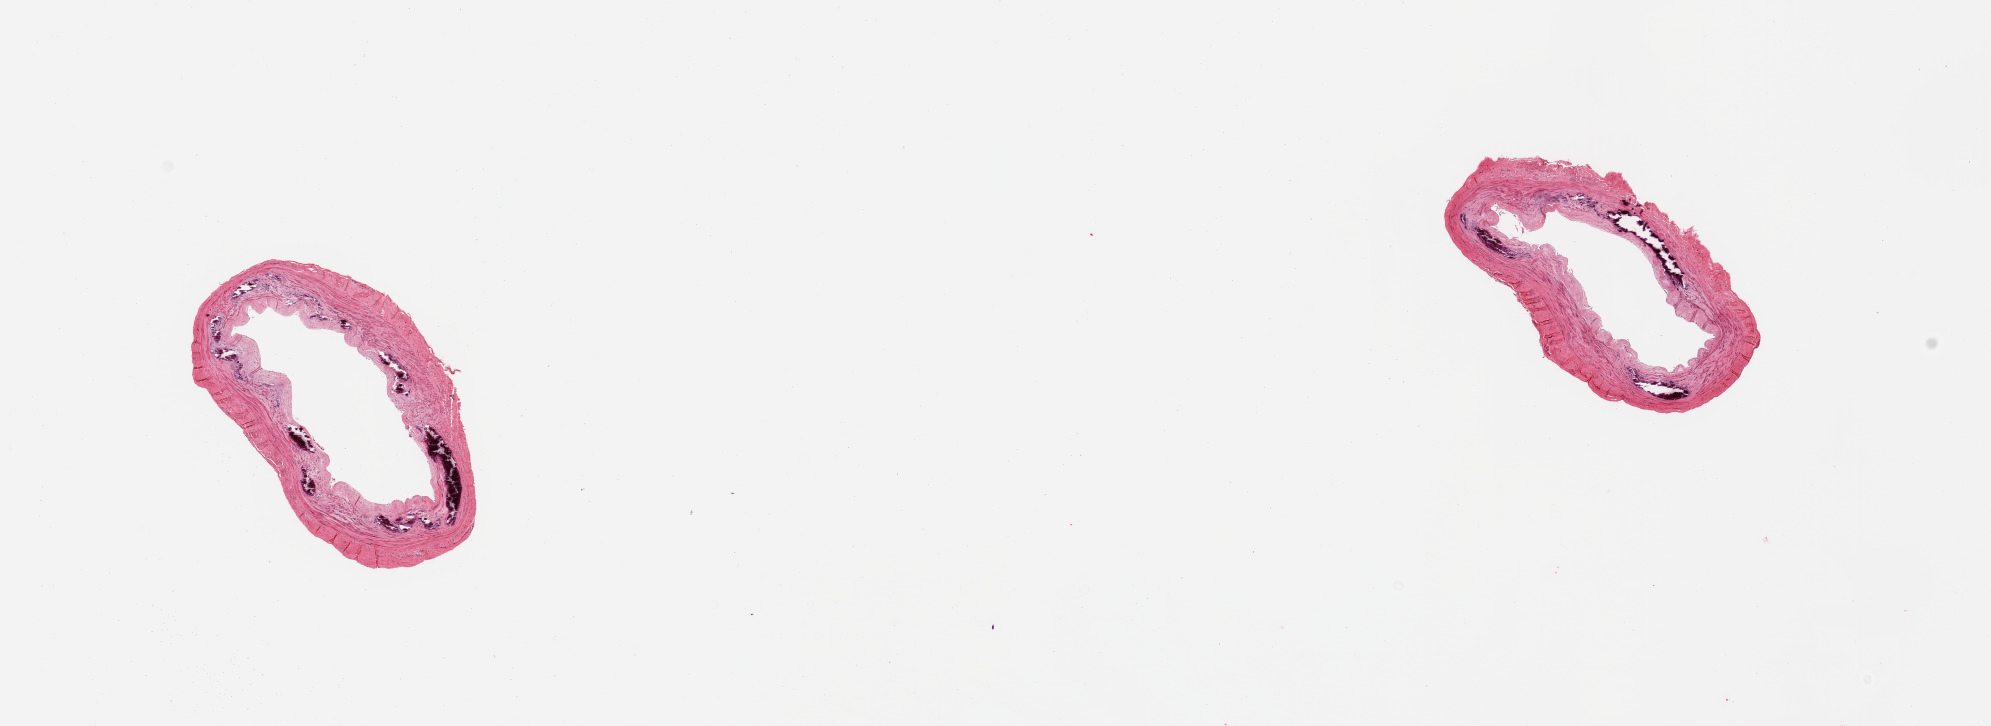
Whole-slide image, hematoxylin and eosin (H&E) stain, shown as a low-resolution overview of the whole scanned area (about 15.8 x 5.7 mm); PAXgene-fixed paraffin-embedded (PFPE) section; section of tibial artery (target tissue); donor tissue sample. Female donor.
Pathologist's review note for this sample: 2 pieces; extensive medial calcification occupies 20%; well trimmed.